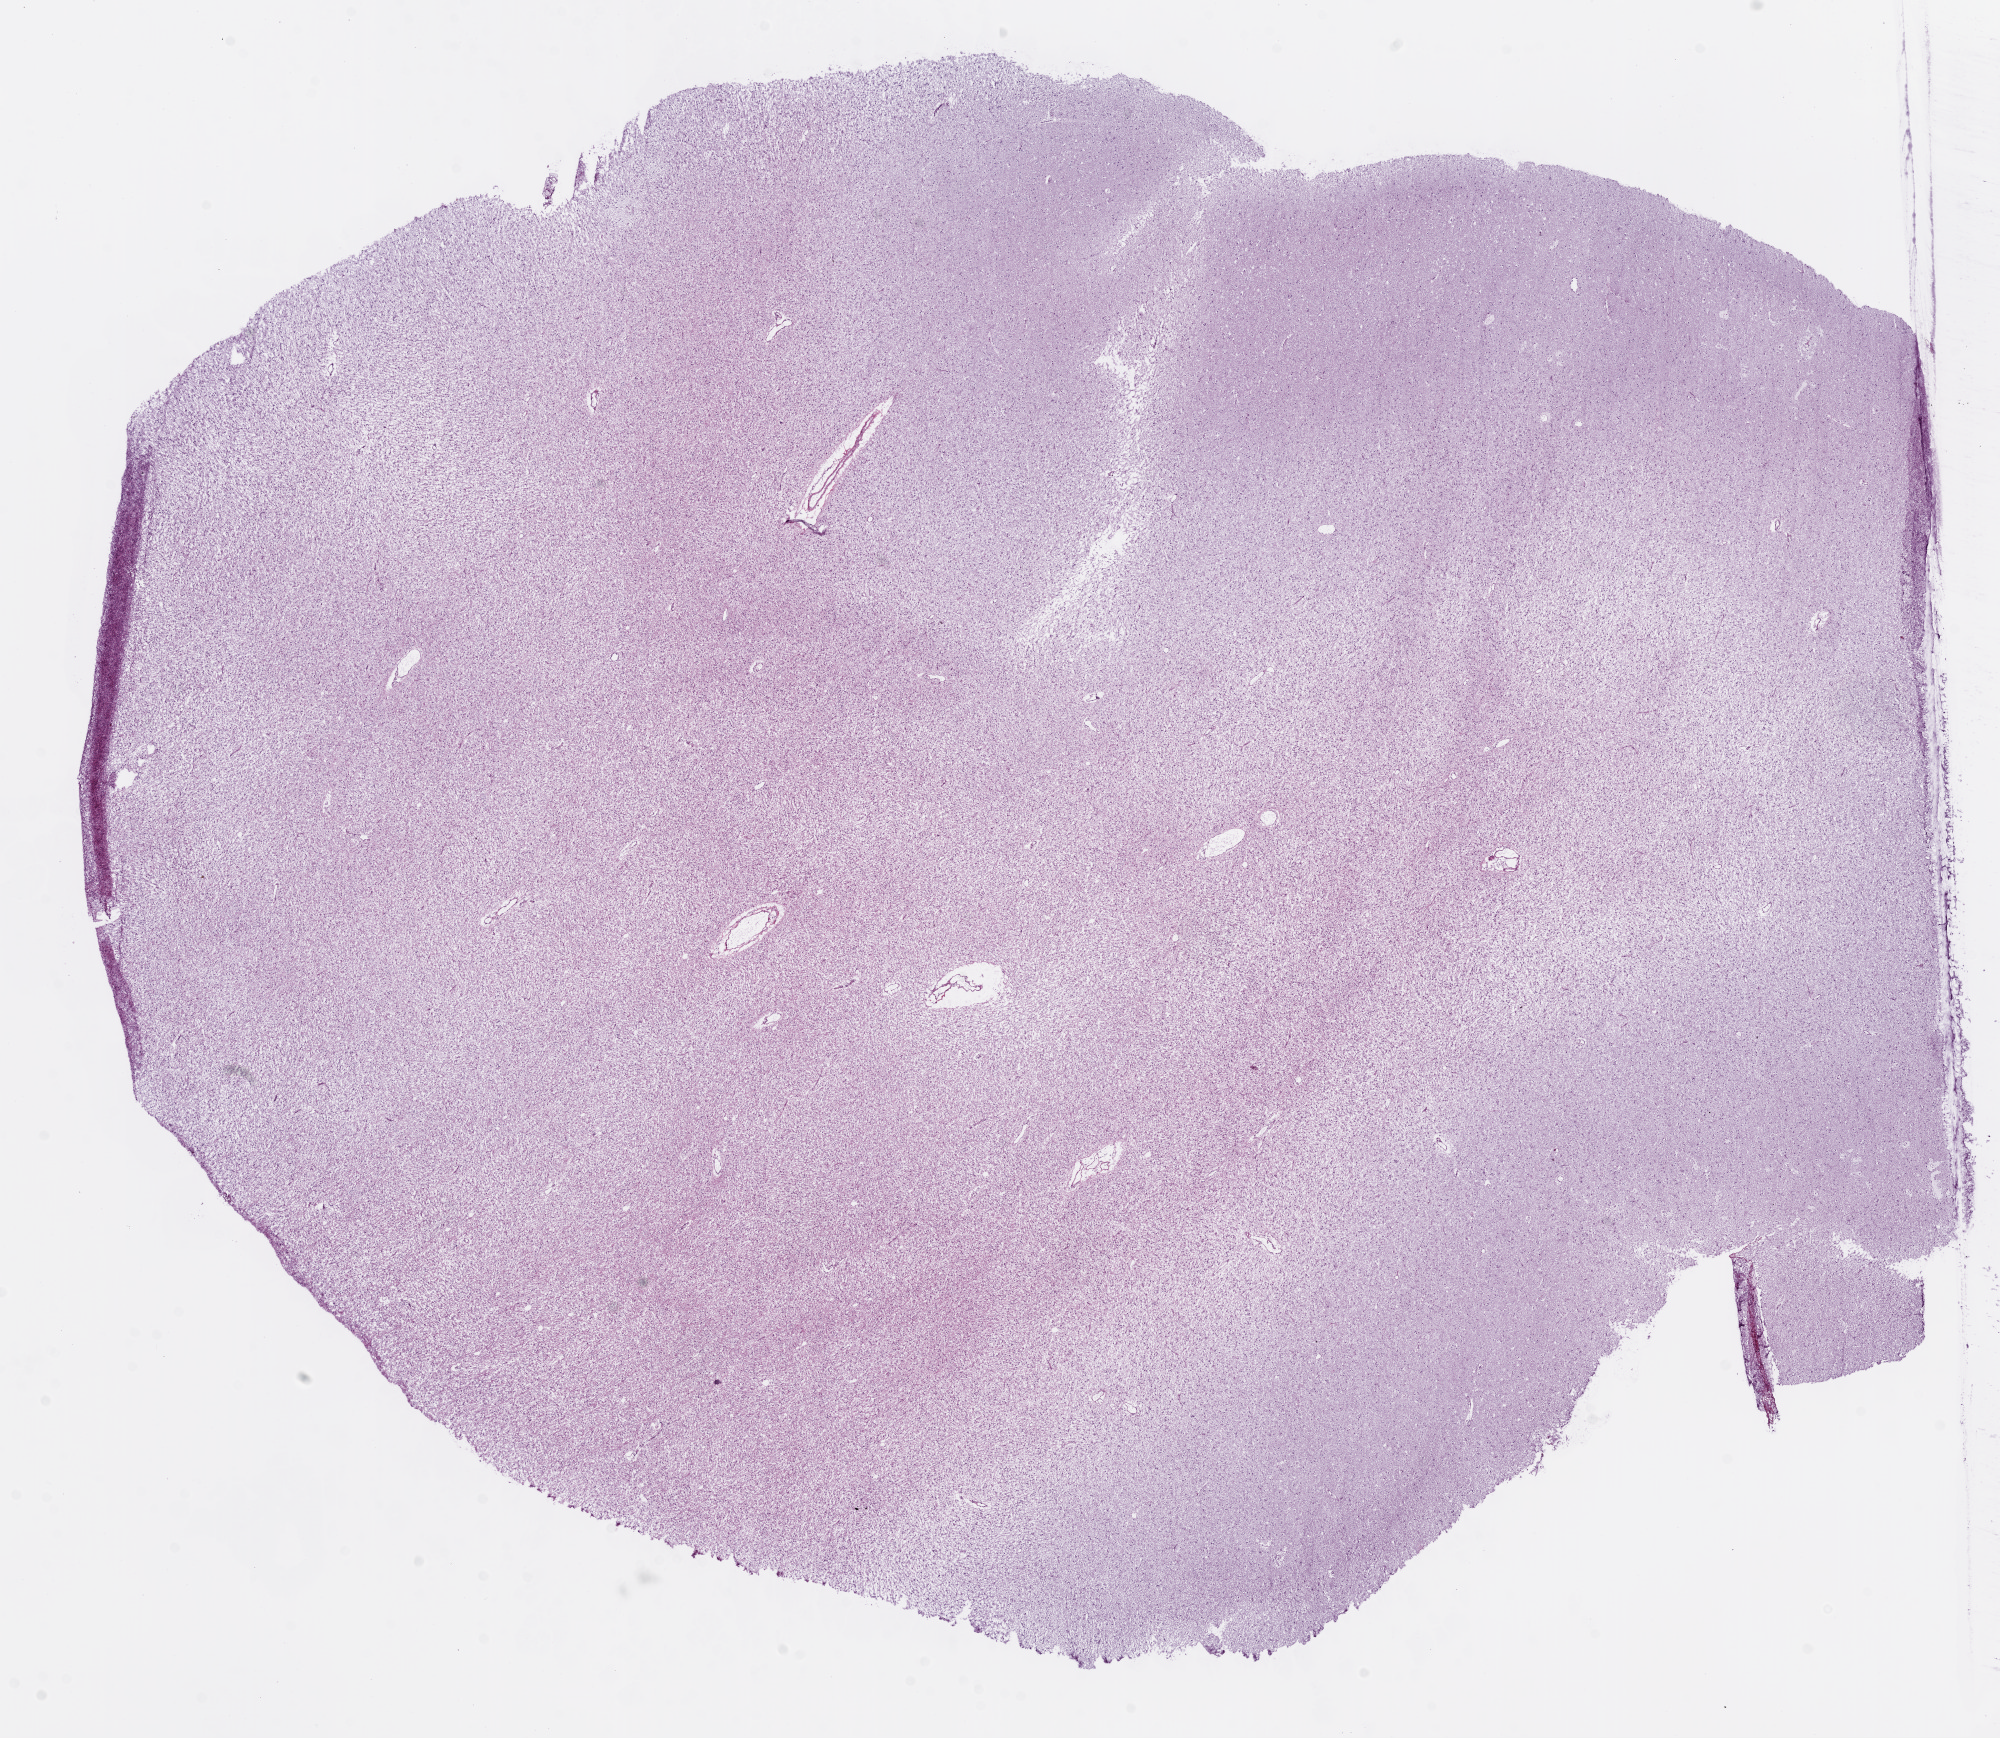
Hematoxylin and eosin (H&E) stained whole-slide image, a low-resolution overview of the entire scanned area, about 16.0 x 13.9 mm (from a 20x scan). Frozen section from the top of the tissue portion. Sample: primary tumour, brain. Male, age 17 years at initial diagnosis. Histologic grade: G2 (moderately differentiated). Composition of this section per pathologist review: tumour cells 100%, tumour nuclei 60%, normal cells 0%, stromal cells 0%, necrosis 0%.
Pathologic diagnosis: Oligodendroglioma, NOS (cerebrum).